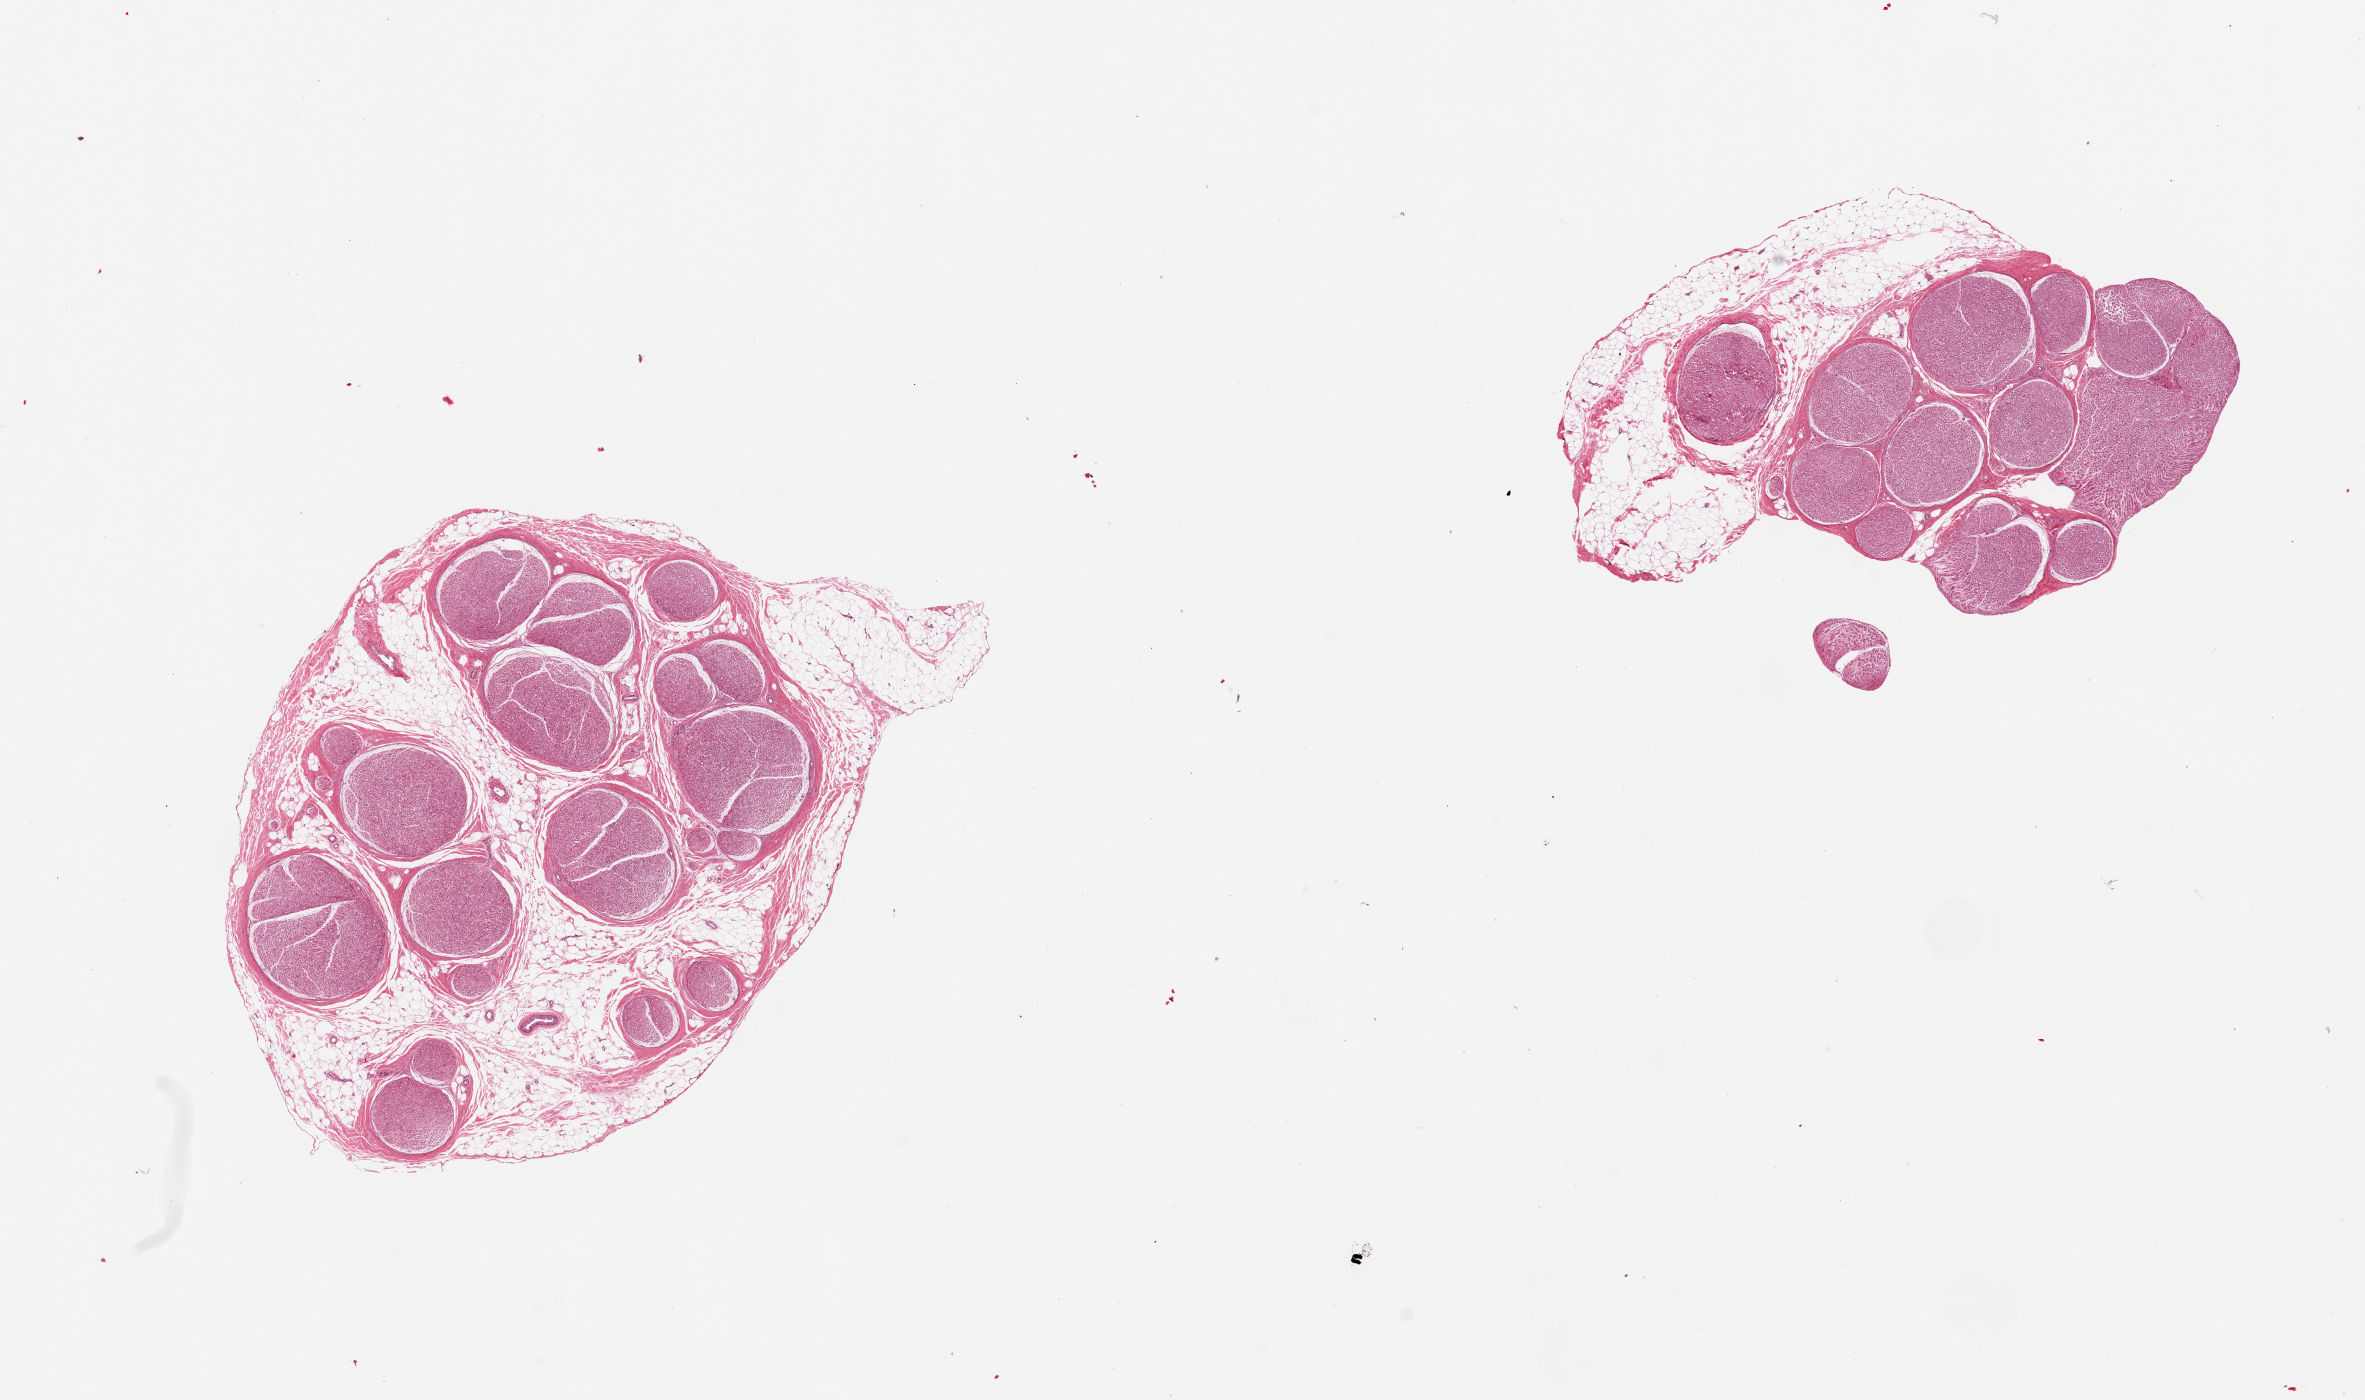
Digitized hematoxylin and eosin (H&E)-stained section, shown as a low-resolution overview of the whole scanned area (about 18.7 x 11.1 mm). PAXgene-fixed, paraffin-embedded tissue. Section of tibial nerve (target tissue). Donor tissue sample. Donor sex: female.
Review note (as recorded): 2 pieces, includes ~40% attached and internal fat.